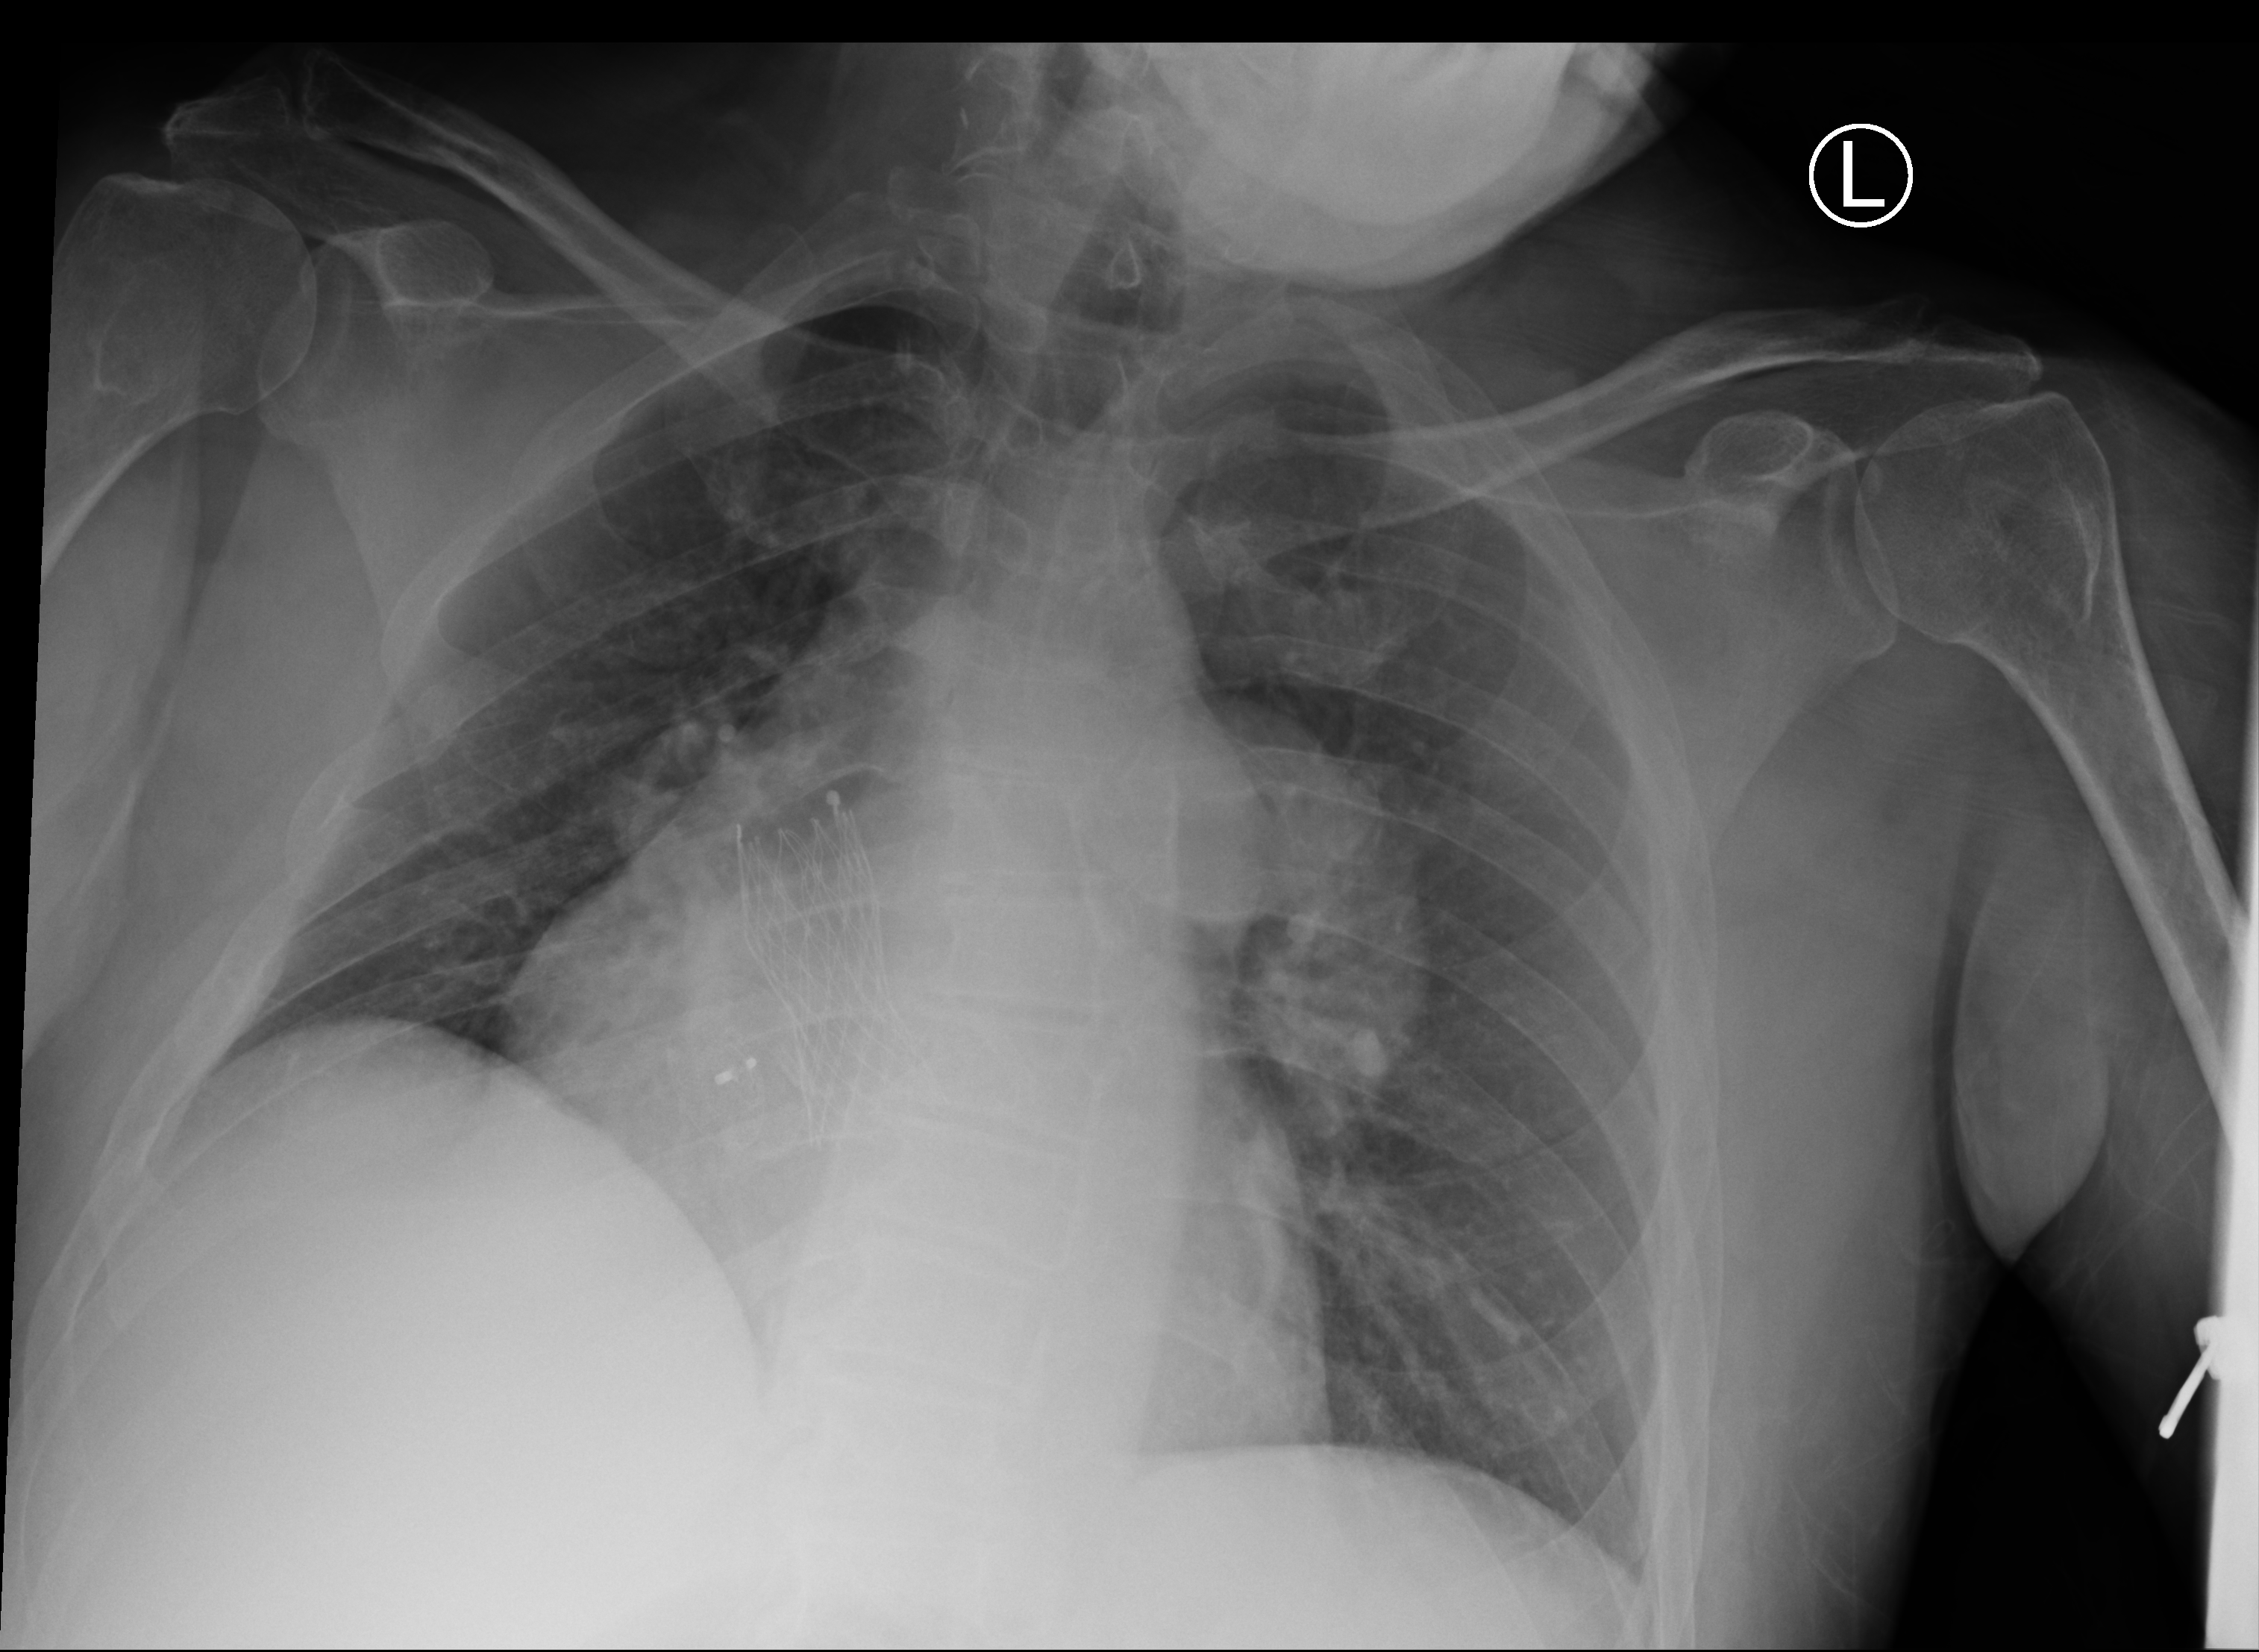
Chest X-ray (portable); anteroposterior (AP) projection. Patient hospitalised with COVID-19; male, aged 60–74 years.
Admission-level facts for this patient (not findings on this image; timing relative to this image not recorded): admitted to intensive care during this hospital stay: no; mechanically ventilated during this hospital stay: no; length of hospital stay: 6 days.